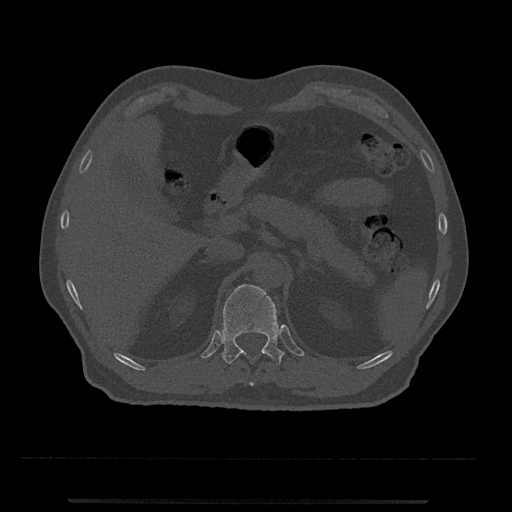
CT including the spine, one axial slice; slice 415 of 797 in the series (ordered by position); 120 kVp; bone window (W 1800 / L 400 HU); 512 × 512 image matrix, field of view 419 × 419 mm. Patient: male, 63 years. Case-level facts recorded for this patient, not image findings: primary cancer: prostate.
Structures marked on this image (semi-automatically segmented with operator editing):
- T11 vertebra: bounding box [x1, y1, x2, y2] px = [240, 352, 269, 386]
- T12 vertebra: [221, 284, 285, 365]